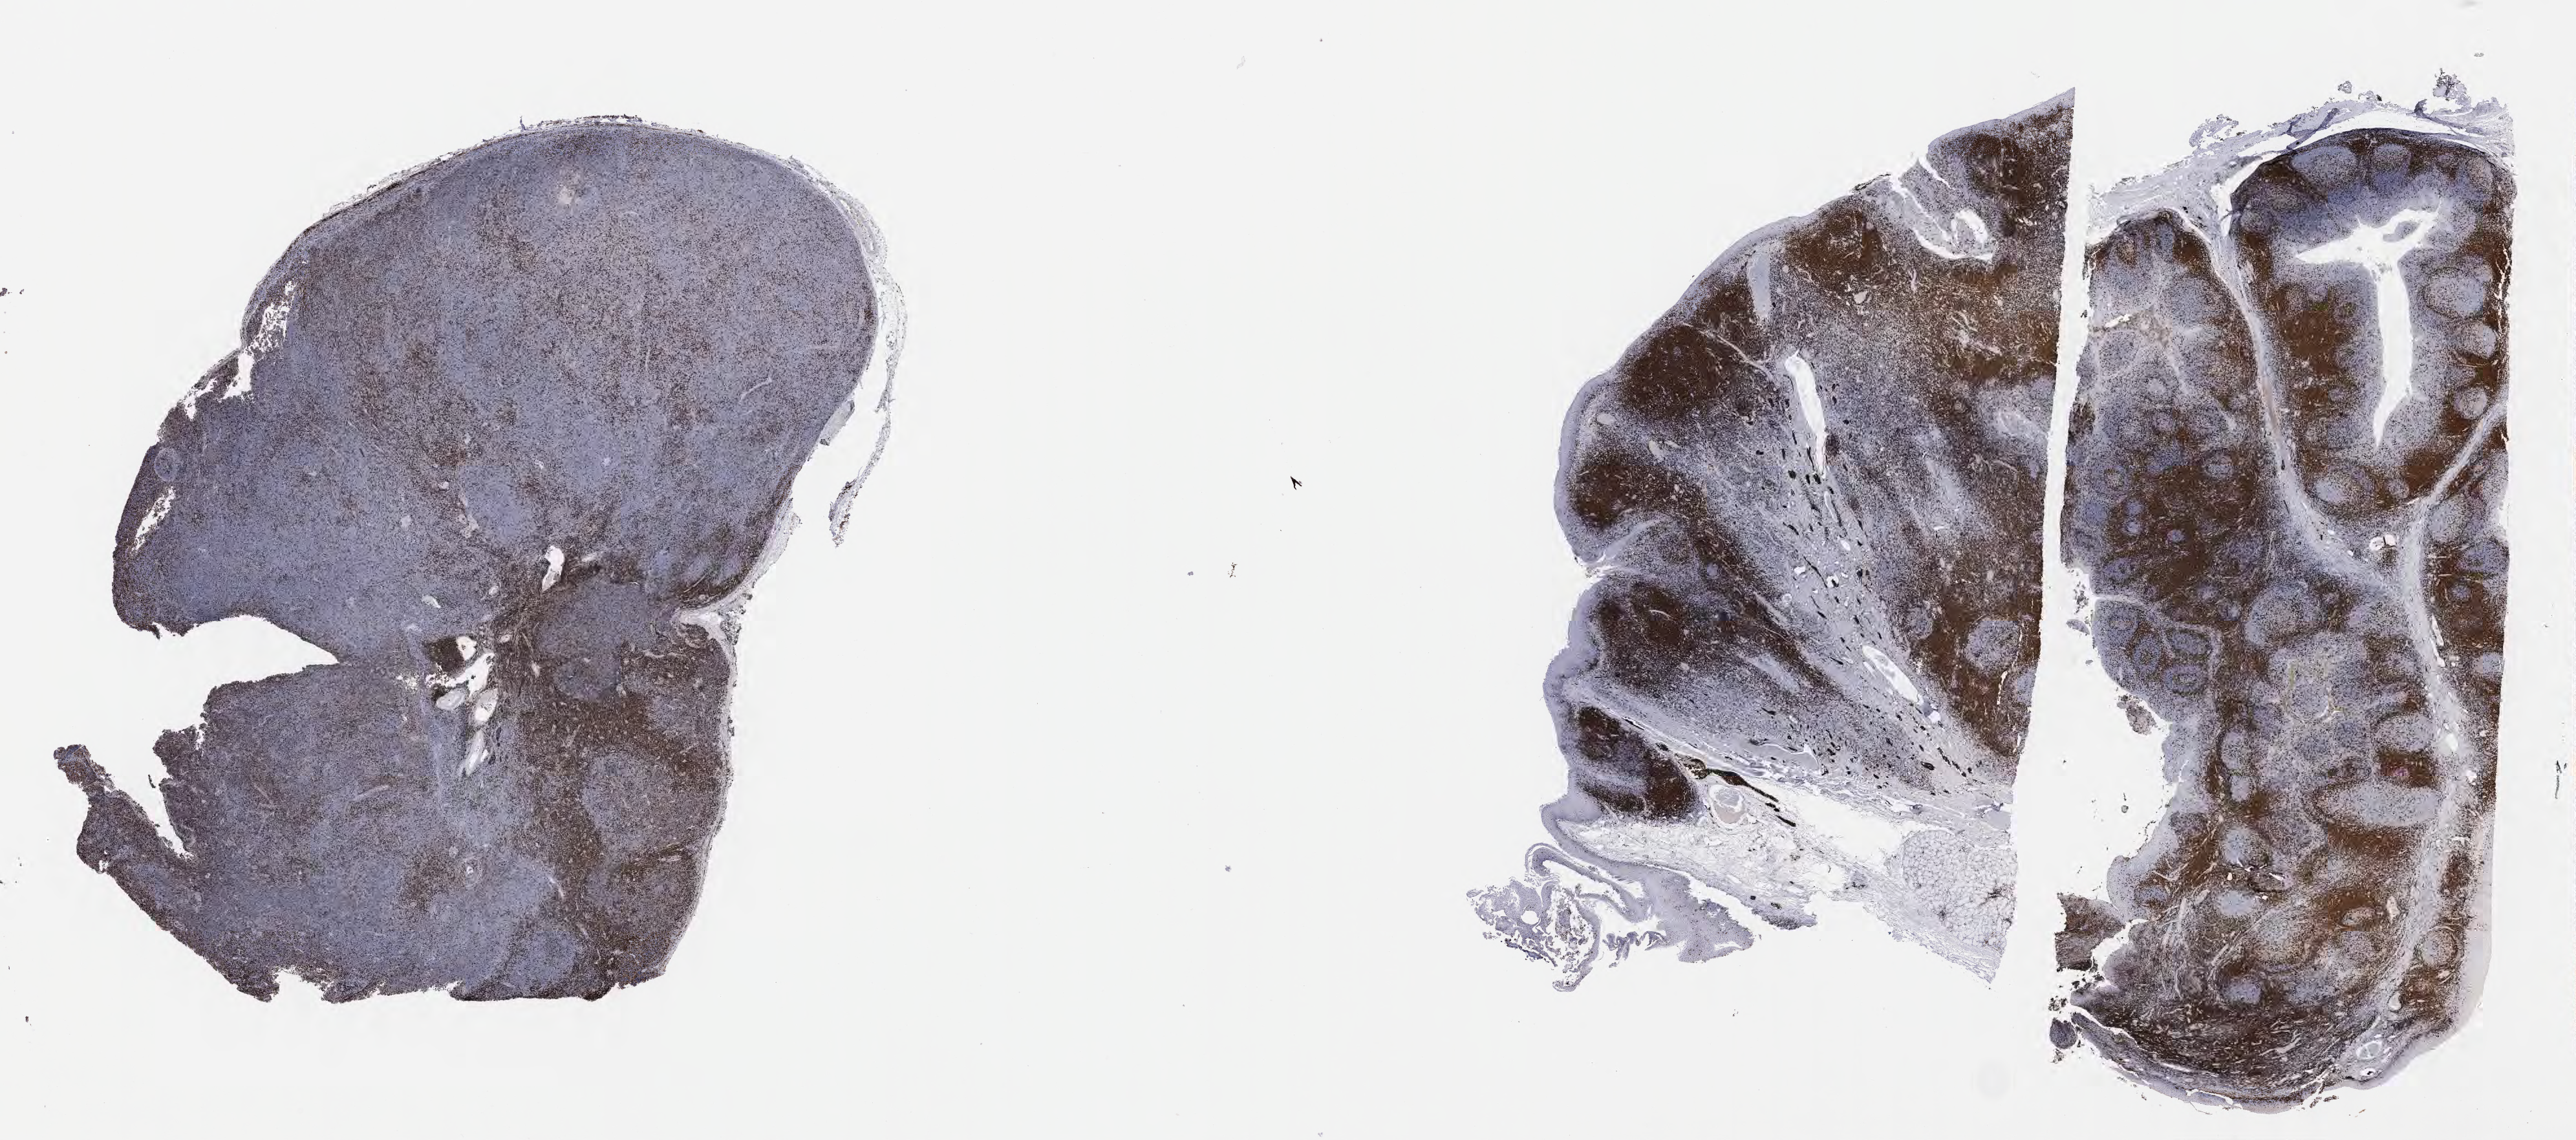
Immunohistochemistry (IHC) whole-slide image stained for CD3, a low-resolution overview of the entire scanned area, about 32.2 x 14.2 mm, specimen: tumor tissue, site: lymph node. Patient male; aged 32.
- diagnosis: Diffuse large B-cell lymphoma, NOS